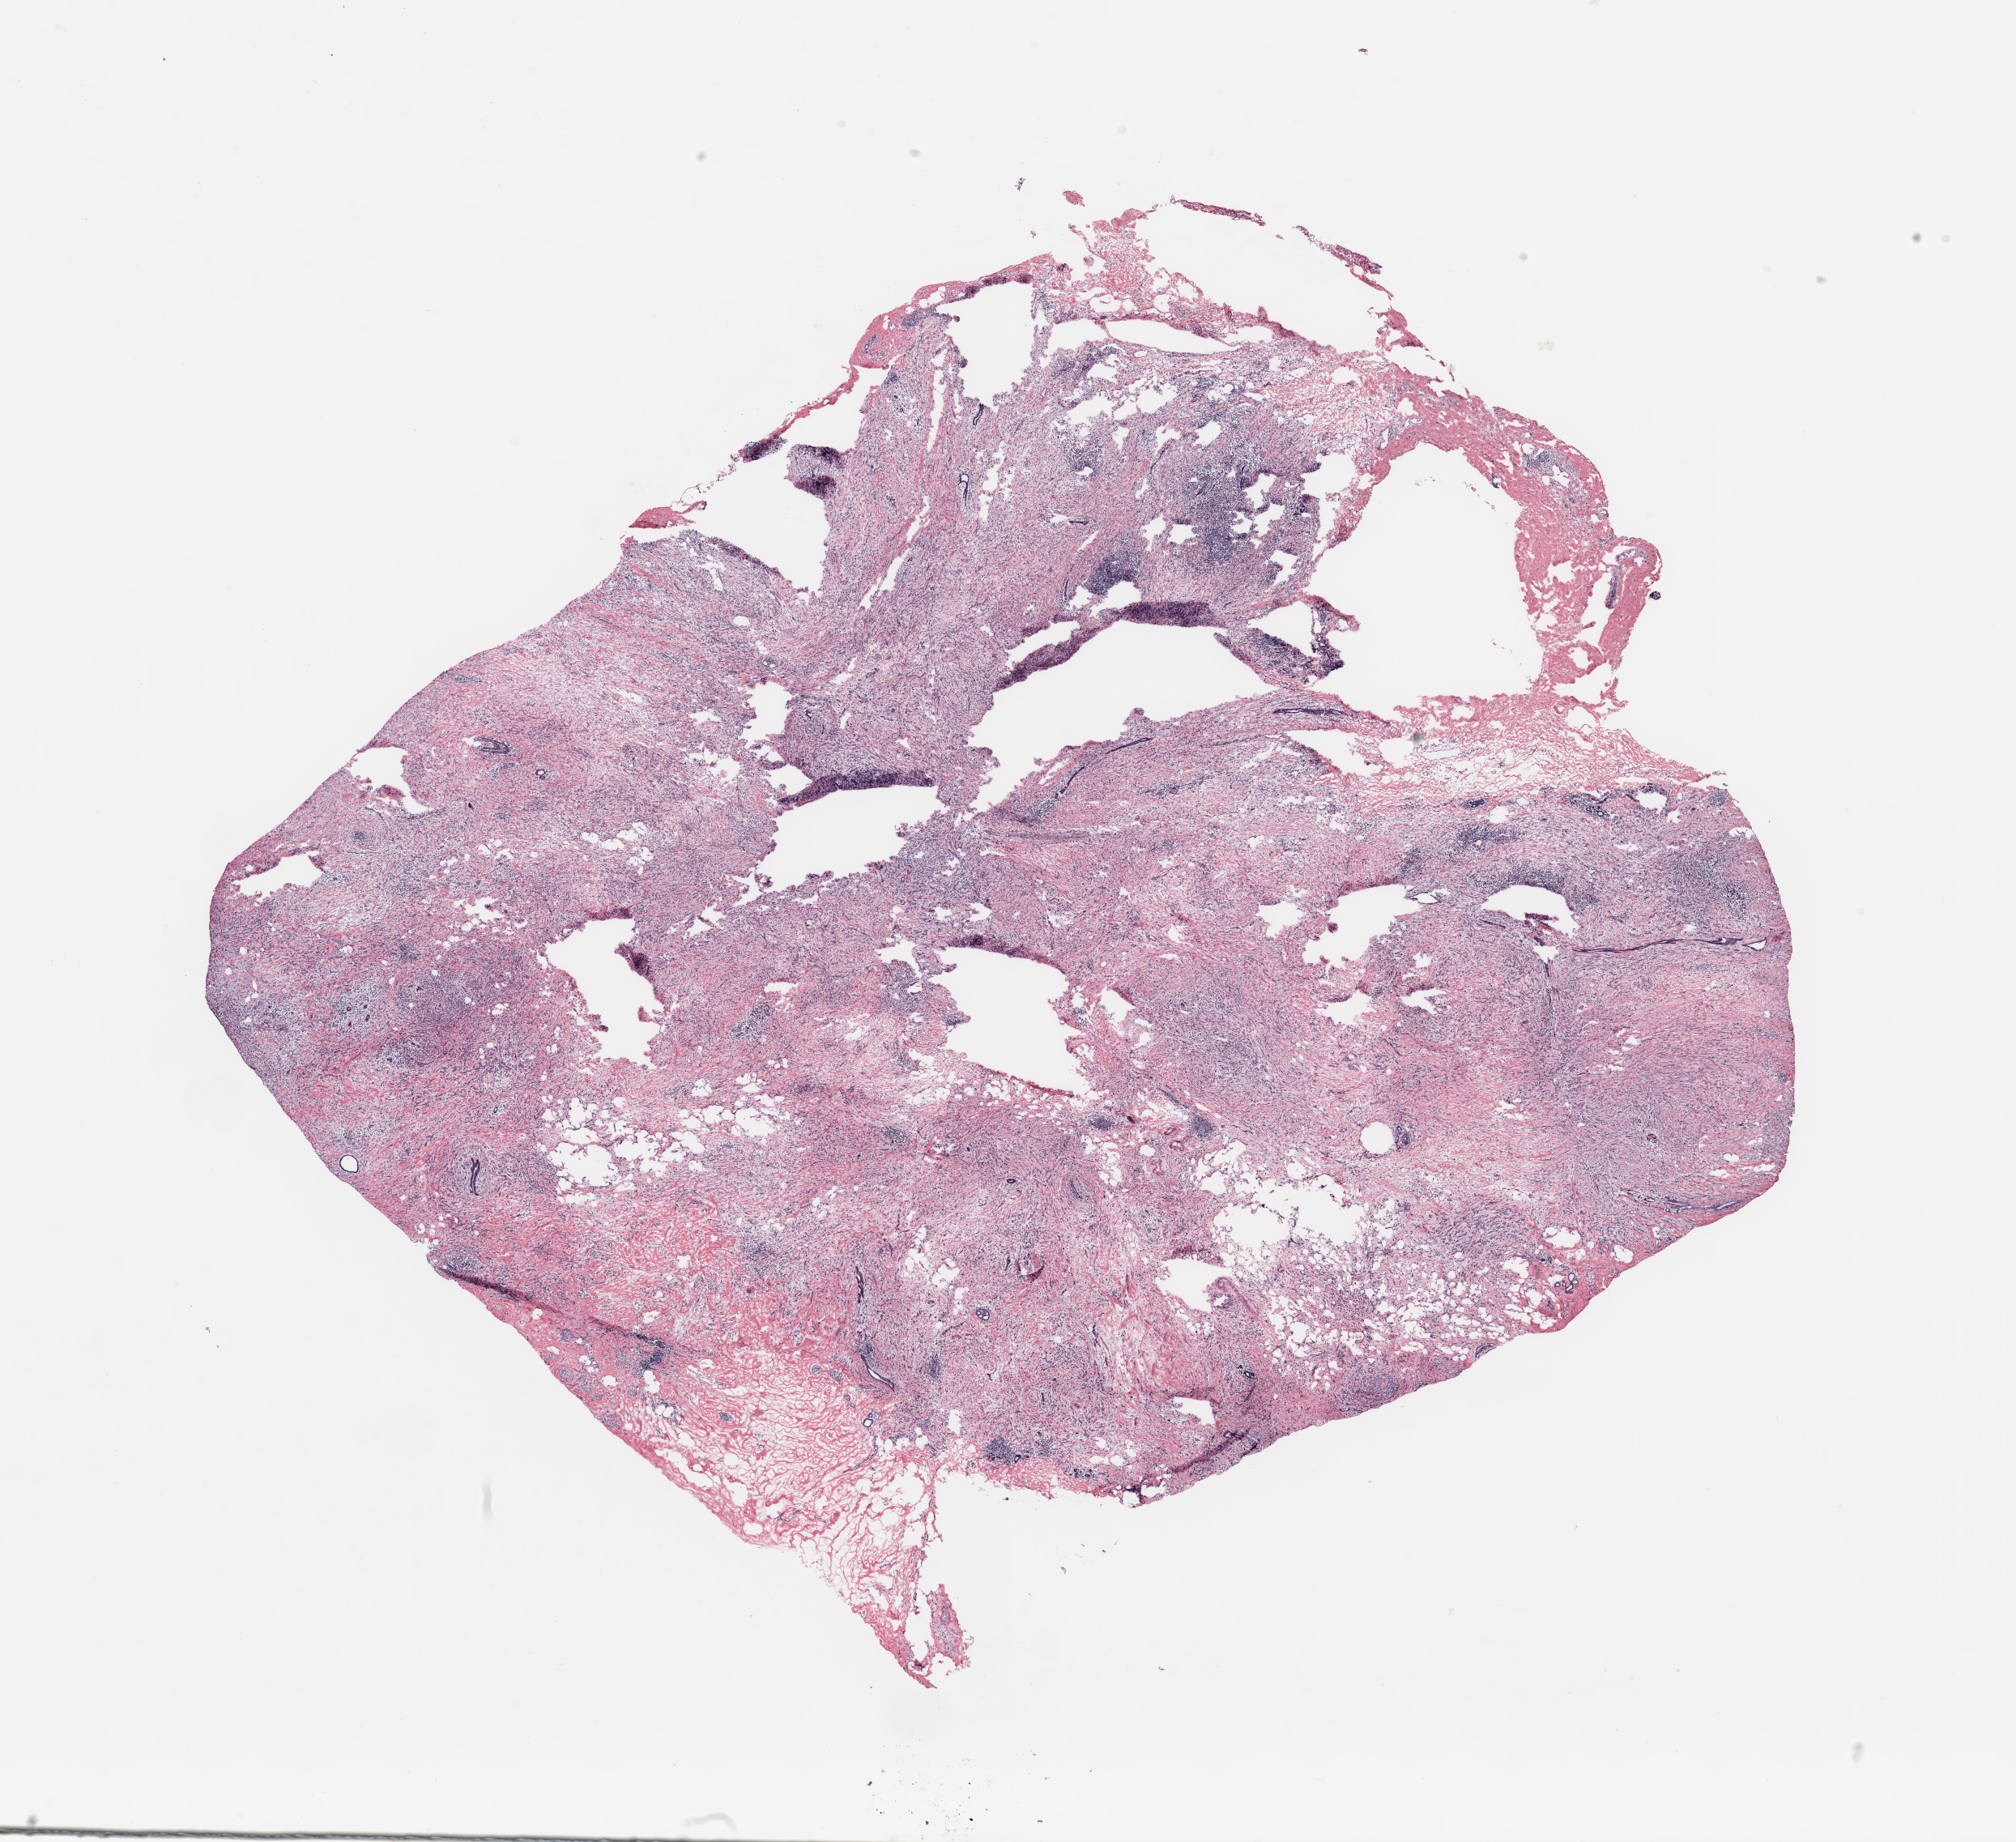
Whole-slide histology image, H&E-stained, low-resolution overview of the scanned area, about 19.7 x 18.0 mm (from a 20x scan); breast, tissue type not recorded.
Patient diagnosis (cohort enrolment): breast cancer (breast).